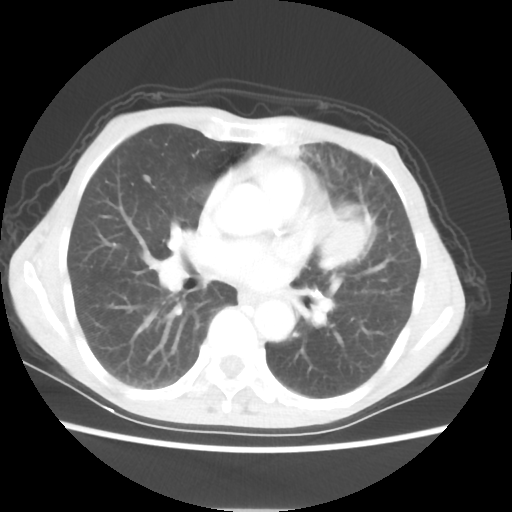
Chest CT, one axial slice. Position 31 of 56 along the scan axis. Reconstruction kernel STANDARD. Lung window (W 1500 / L -600 HU). 512 × 512 image matrix, field of view 331 × 331 mm. Patient: female, 60 years. Case-level facts recorded for this patient, not image findings: clinical TNM (as recorded): T4 N1 M0.
Outlined on this slice (rectangle marked by the reading radiologist):
- lung tumour (recorded histology: adenocarcinoma): box from (x=313, y=202) to (x=373, y=274) px